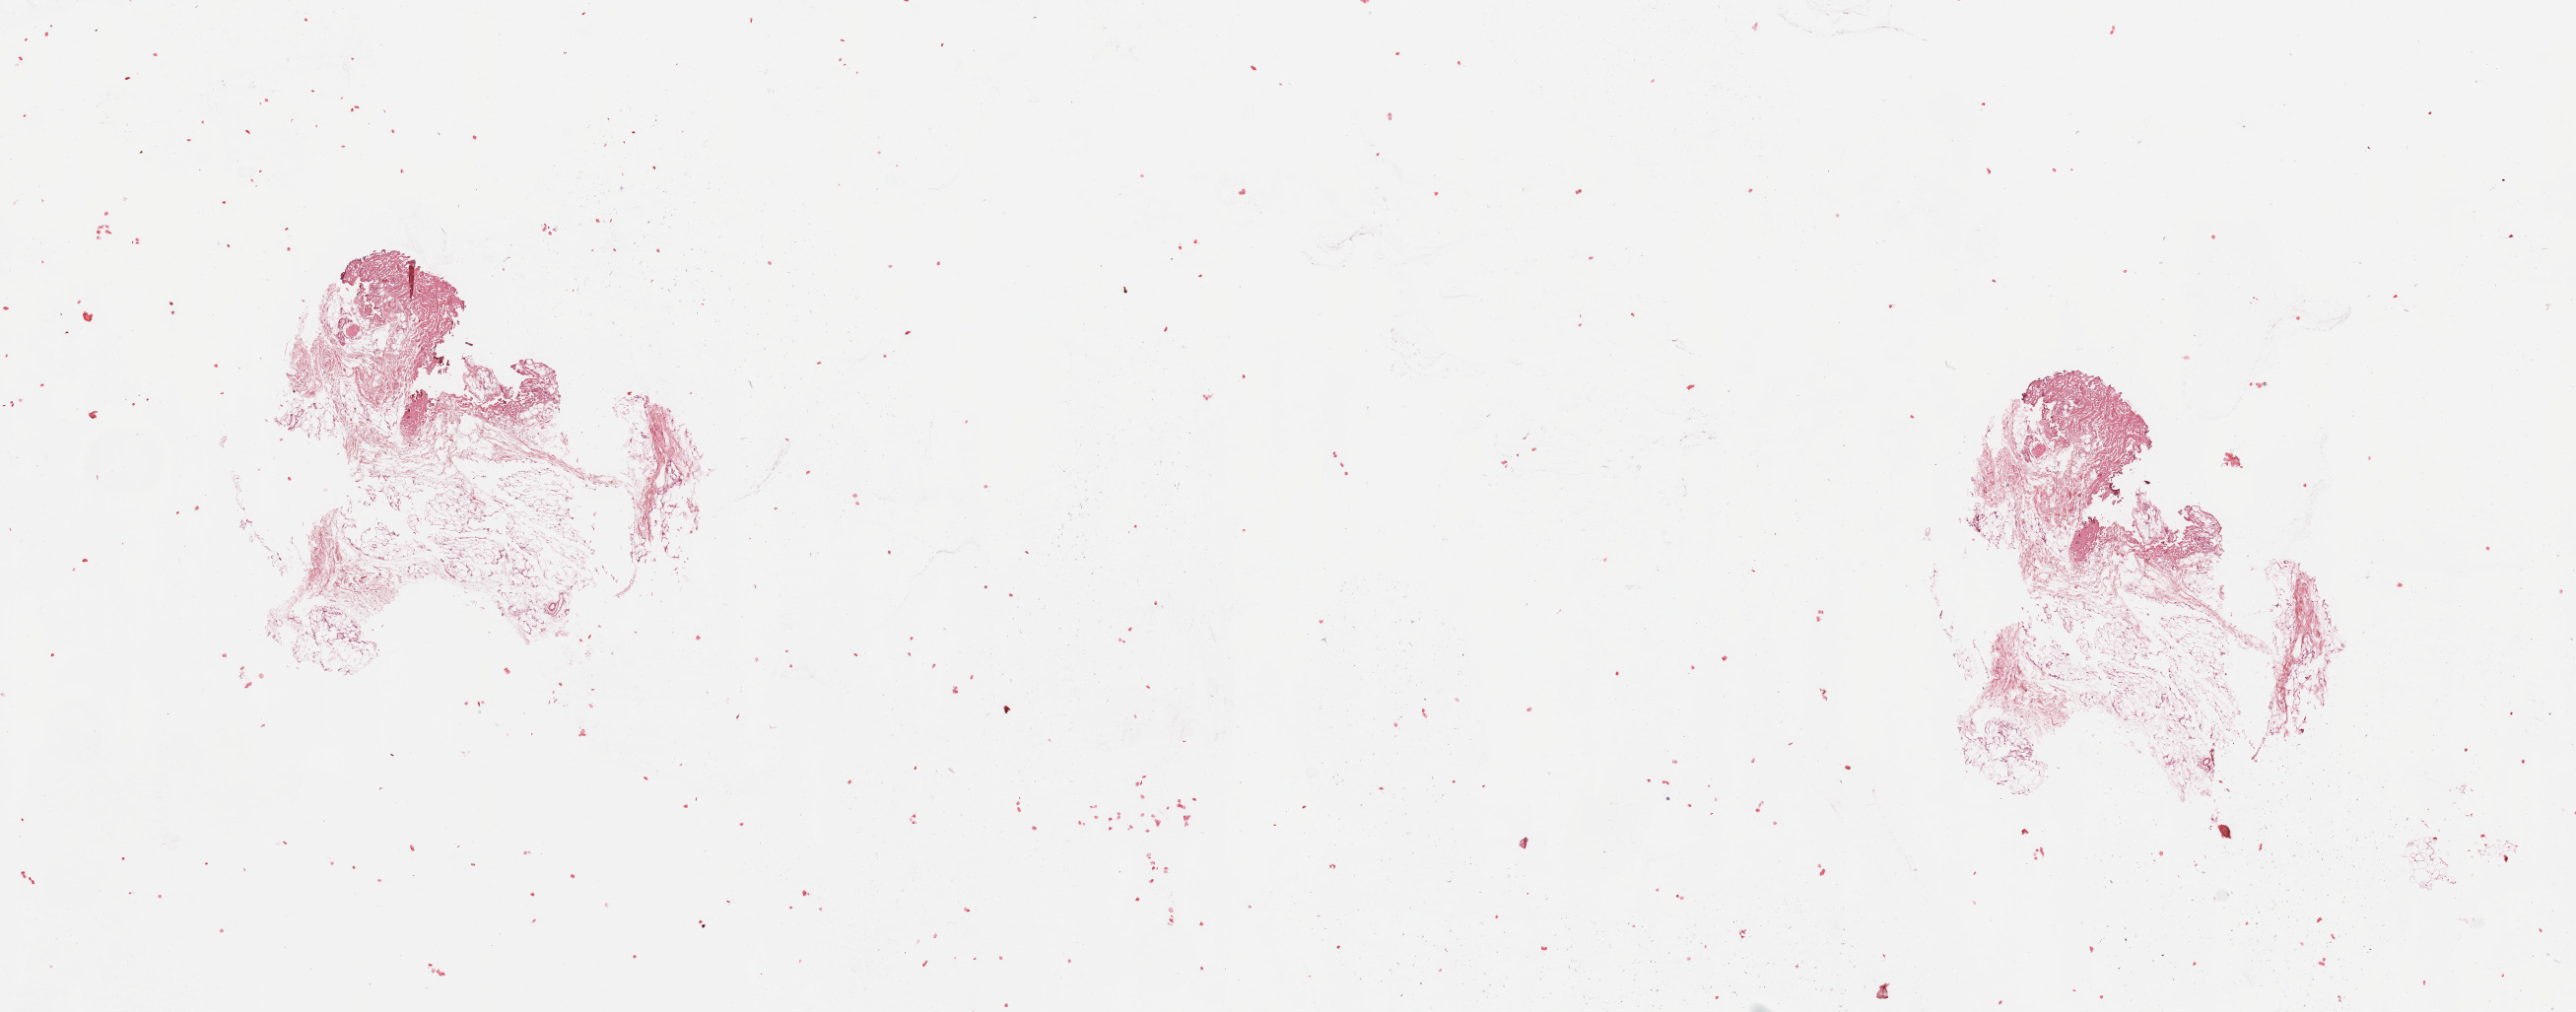
Digitized Hematoxylin and eosin (H&E) stained tissue section (whole slide) — shown as a low-resolution overview of the whole scanned area (about 20.7 x 8.1 mm, slide scanned at 20x); head and neck, tissue type not recorded. Male, 58 y/o.
Patient diagnosis: Squamous cell carcinoma, NOS (overlapping lesion of lip, oral cavity and pharynx).